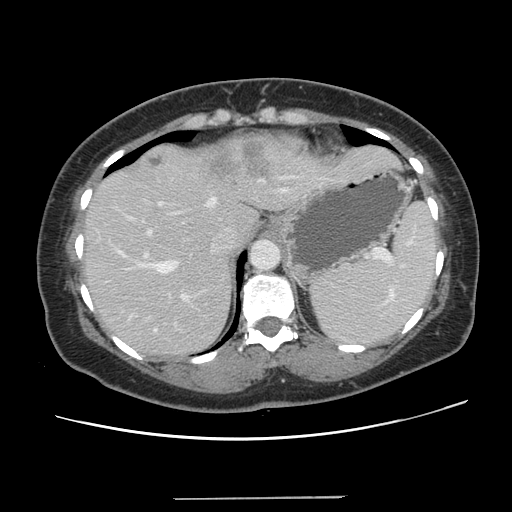
Contrast-enhanced abdominal CT, one axial slice. Slice 100 of 141 in the series (ordered by position). 120 kVp. Intravenous contrast given. Soft-tissue window (W 400 / L 40 HU). 2.5 mm slice thickness. 512 × 512 image matrix, field of view 366 × 366 mm. Female patient, age 53 years. From the clinical record (not read from this slice): diagnosis: colorectal cancer liver metastases, imaged before liver resection; multiple liver metastases: no; largest metastasis: 14.5 cm; disease in both lobes: yes.
Structures marked on this image (expert manual segmentation):
- hepatic veins: bounding box (x1, y1, x2, y2) in pixels: (121, 175, 296, 331)
- liver: (84, 137, 398, 356)
- planned liver remnant (the part of the liver to remain after resection): (84, 209, 260, 356)
- portal vein (with intrahepatic branches): (125, 189, 284, 303)
- liver metastasis: (148, 156, 164, 168)
- liver metastasis: (211, 143, 271, 183)